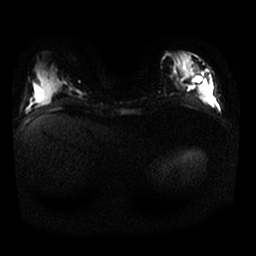
Breast MRI, one axial slice; position 11 of 25 along the scan axis; diffusion-weighted series; image 2 of 4 stored at this slice position (different b-values; order by instance number); 1.5 T; 4 mm slice thickness; 256 × 256 image matrix. Female patient.
Structures marked on this image (expert manual segmentation):
- tumour on diffusion-weighted imaging: bounding box [x1, y1, x2, y2] px = [187, 66, 213, 105]